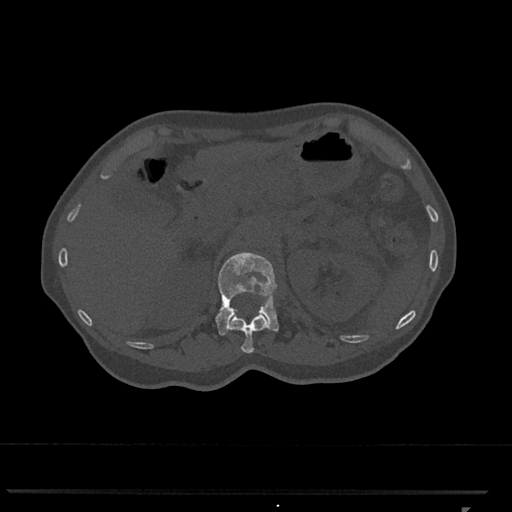
CT including the spine, one axial slice; slice 427 of 793 in the series (ordered by position); reconstruction kernel Br40s/3; bone window (W 1800 / L 400 HU); 0.5 mm slice thickness; 512 × 512 image matrix, field of view 380 × 380 mm. Female patient, age 62 years. Case-level facts recorded for this patient, not image findings: primary cancer: renal.
Structures marked on this image (semi-automatically segmented with operator editing):
- L1 vertebra: bounding box (x1, y1, x2, y2) in pixels: (215, 253, 279, 335)
- T12 vertebra: (229, 312, 268, 354)